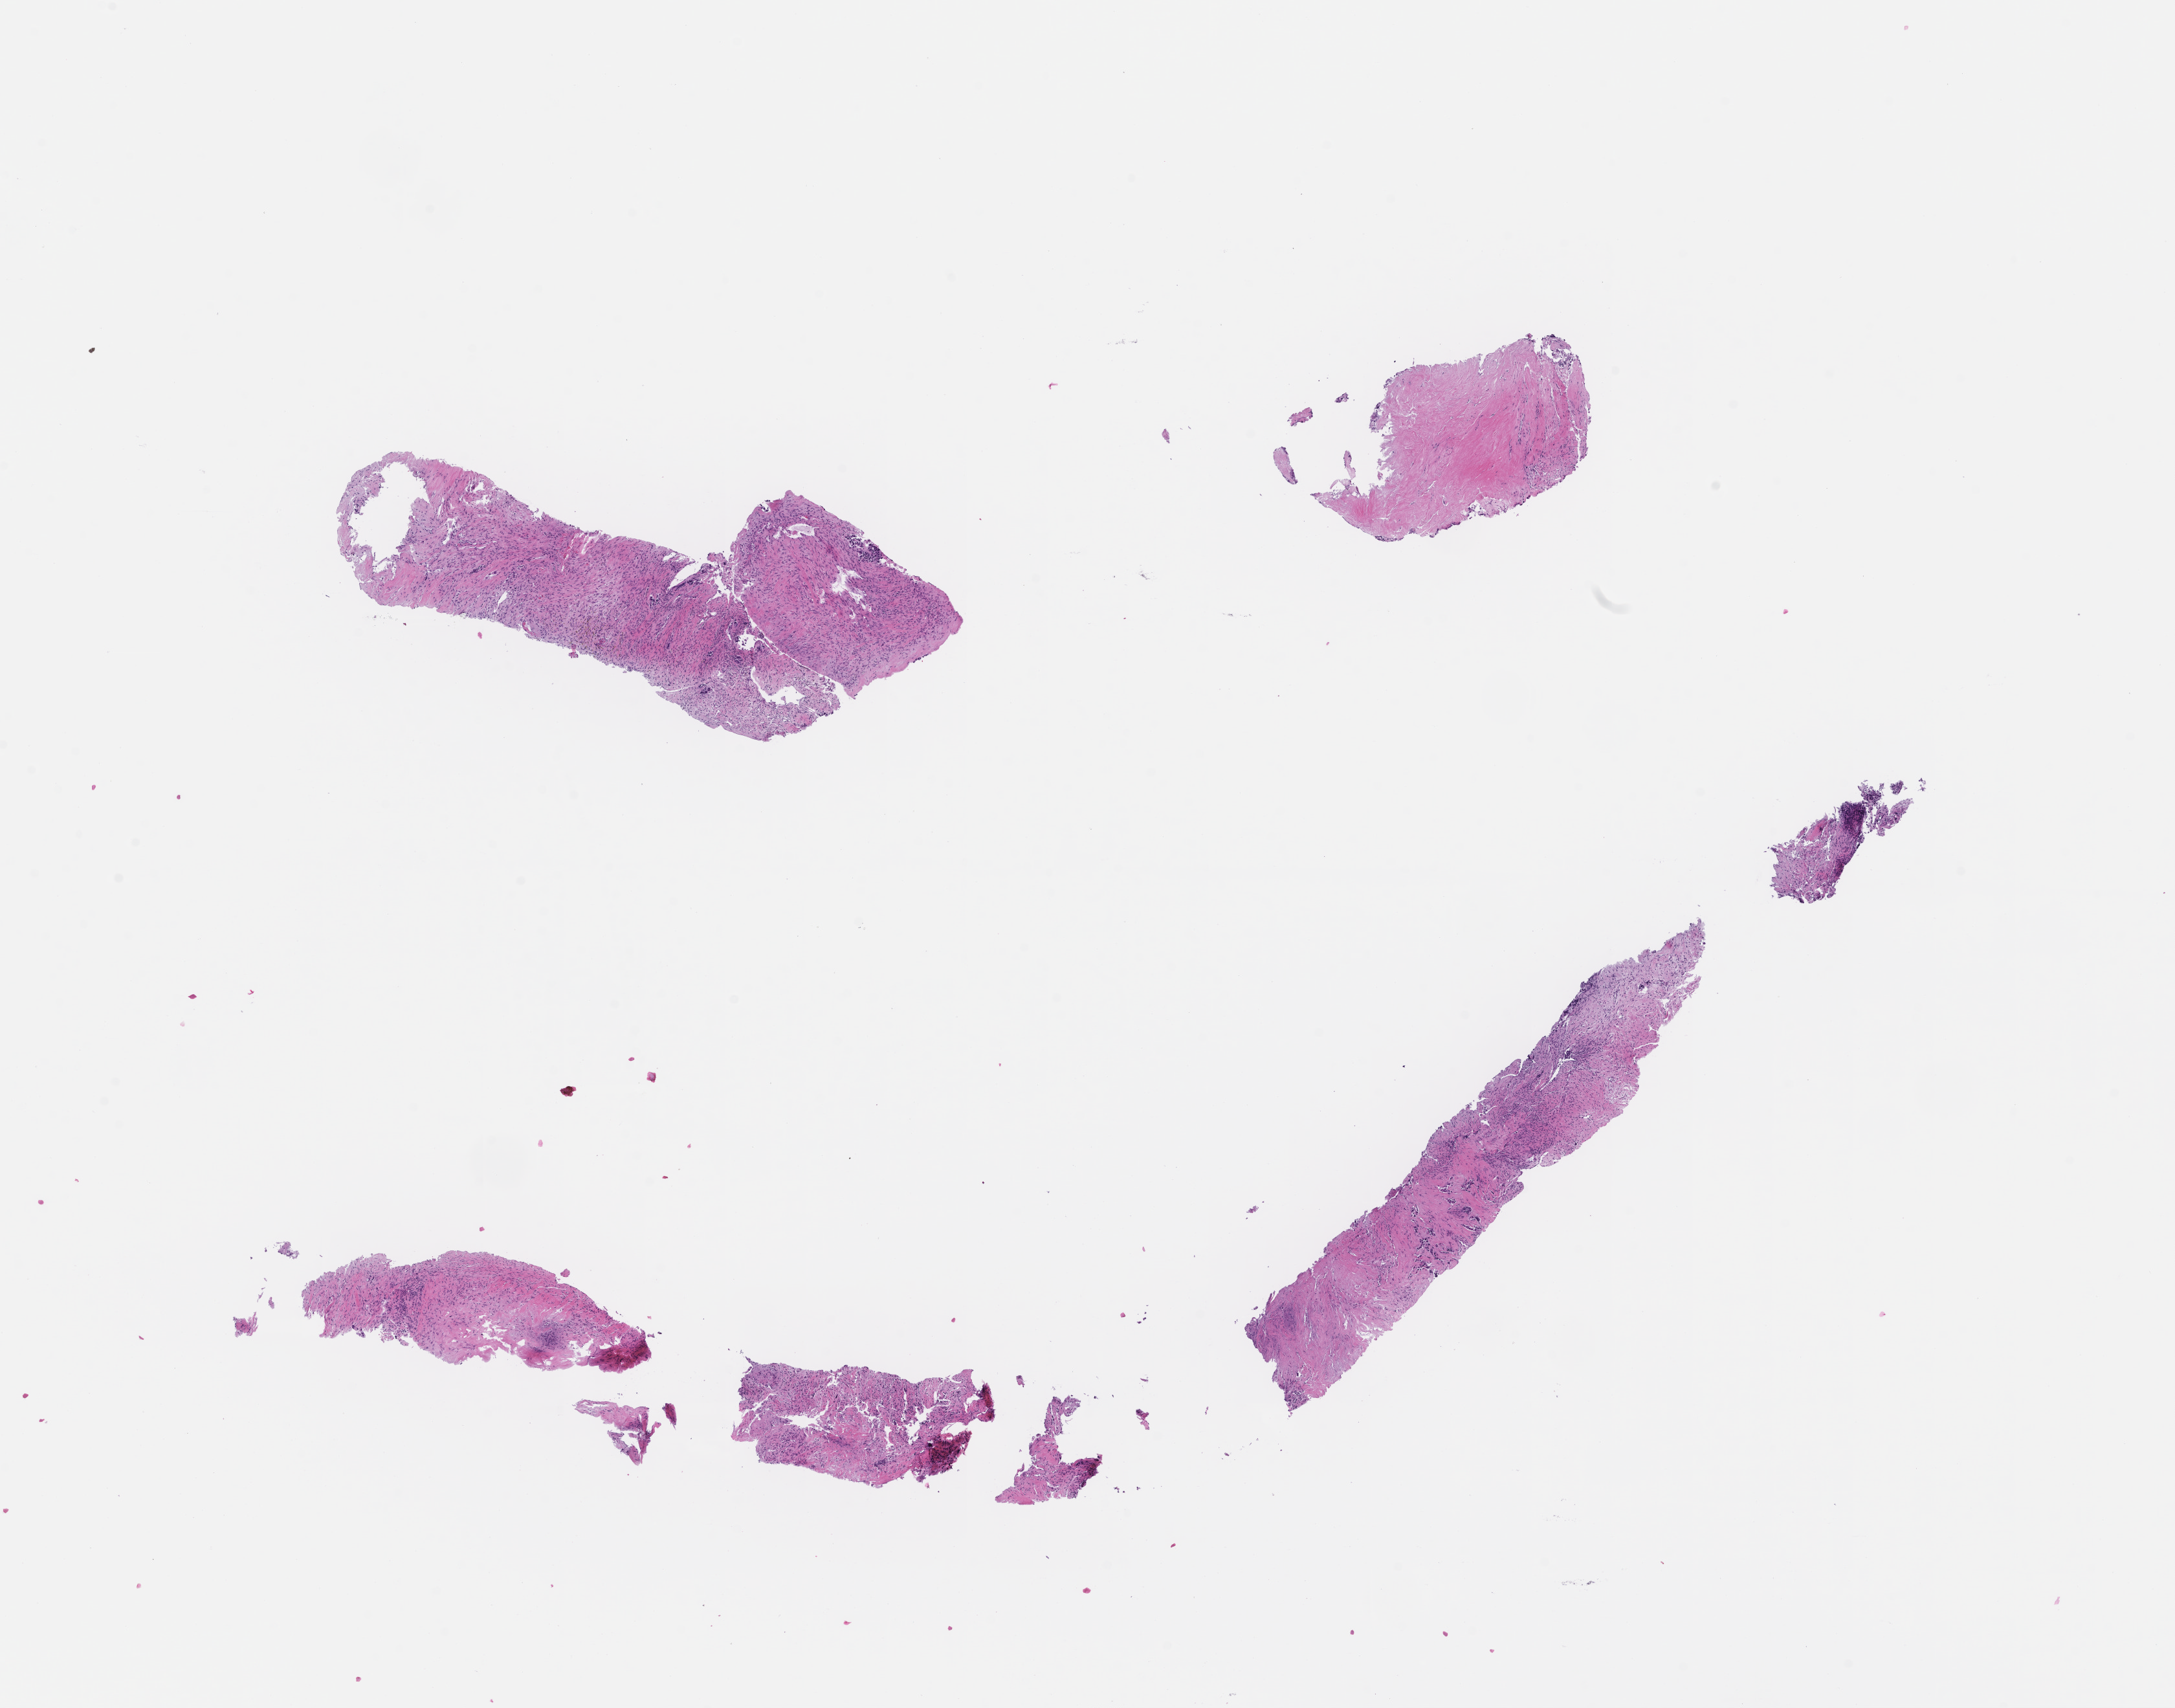
Haematoxylin and eosin whole-slide image — shown as a low-resolution overview of the whole scanned area (about 13.6 x 10.7 mm); formalin-fixed, paraffin-embedded (FFPE) tissue; tissue site: lung. Patient sex: female.
- this section: primary tumour tissue
- diagnosis: Non-Small Cell Lung Carcinoma